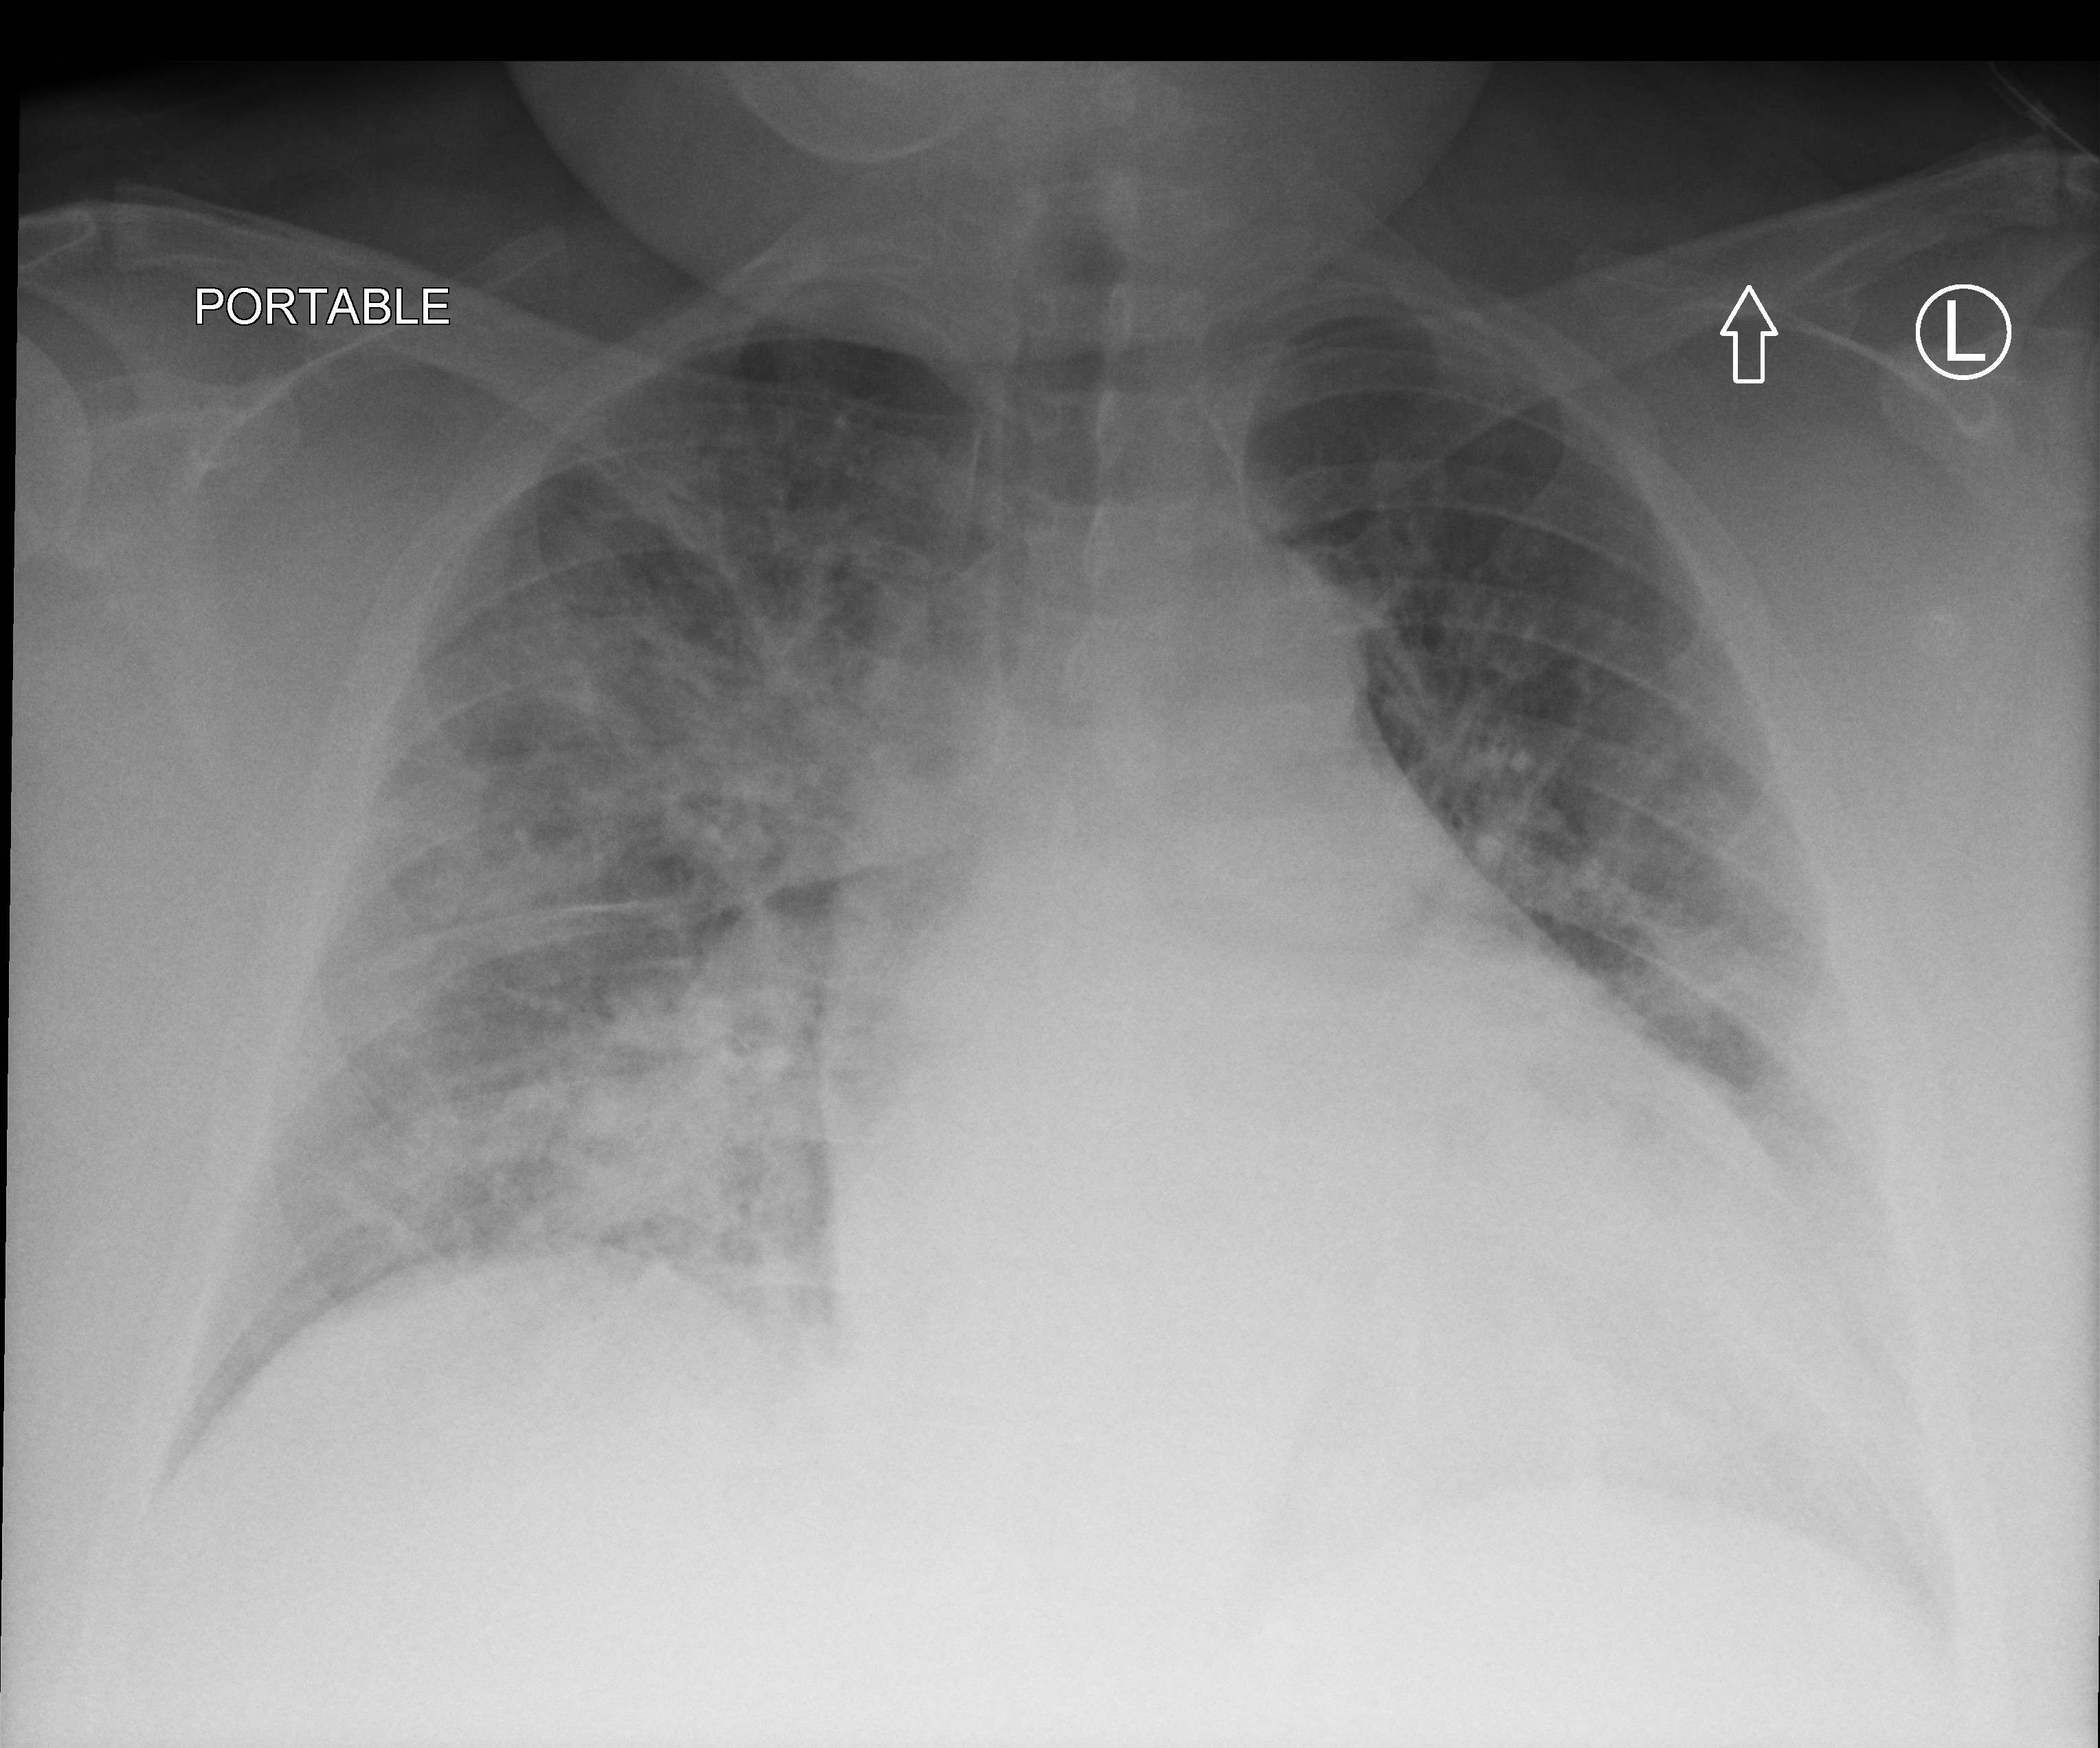
Bedside chest radiograph (computed radiography), anteroposterior (AP) projection. Male patient hospitalised with COVID-19, age 18–59 years.
Hospital-stay facts (about this admission, not read from this image; timing relative to this image not recorded):
- admitted to intensive care during this hospital stay: no